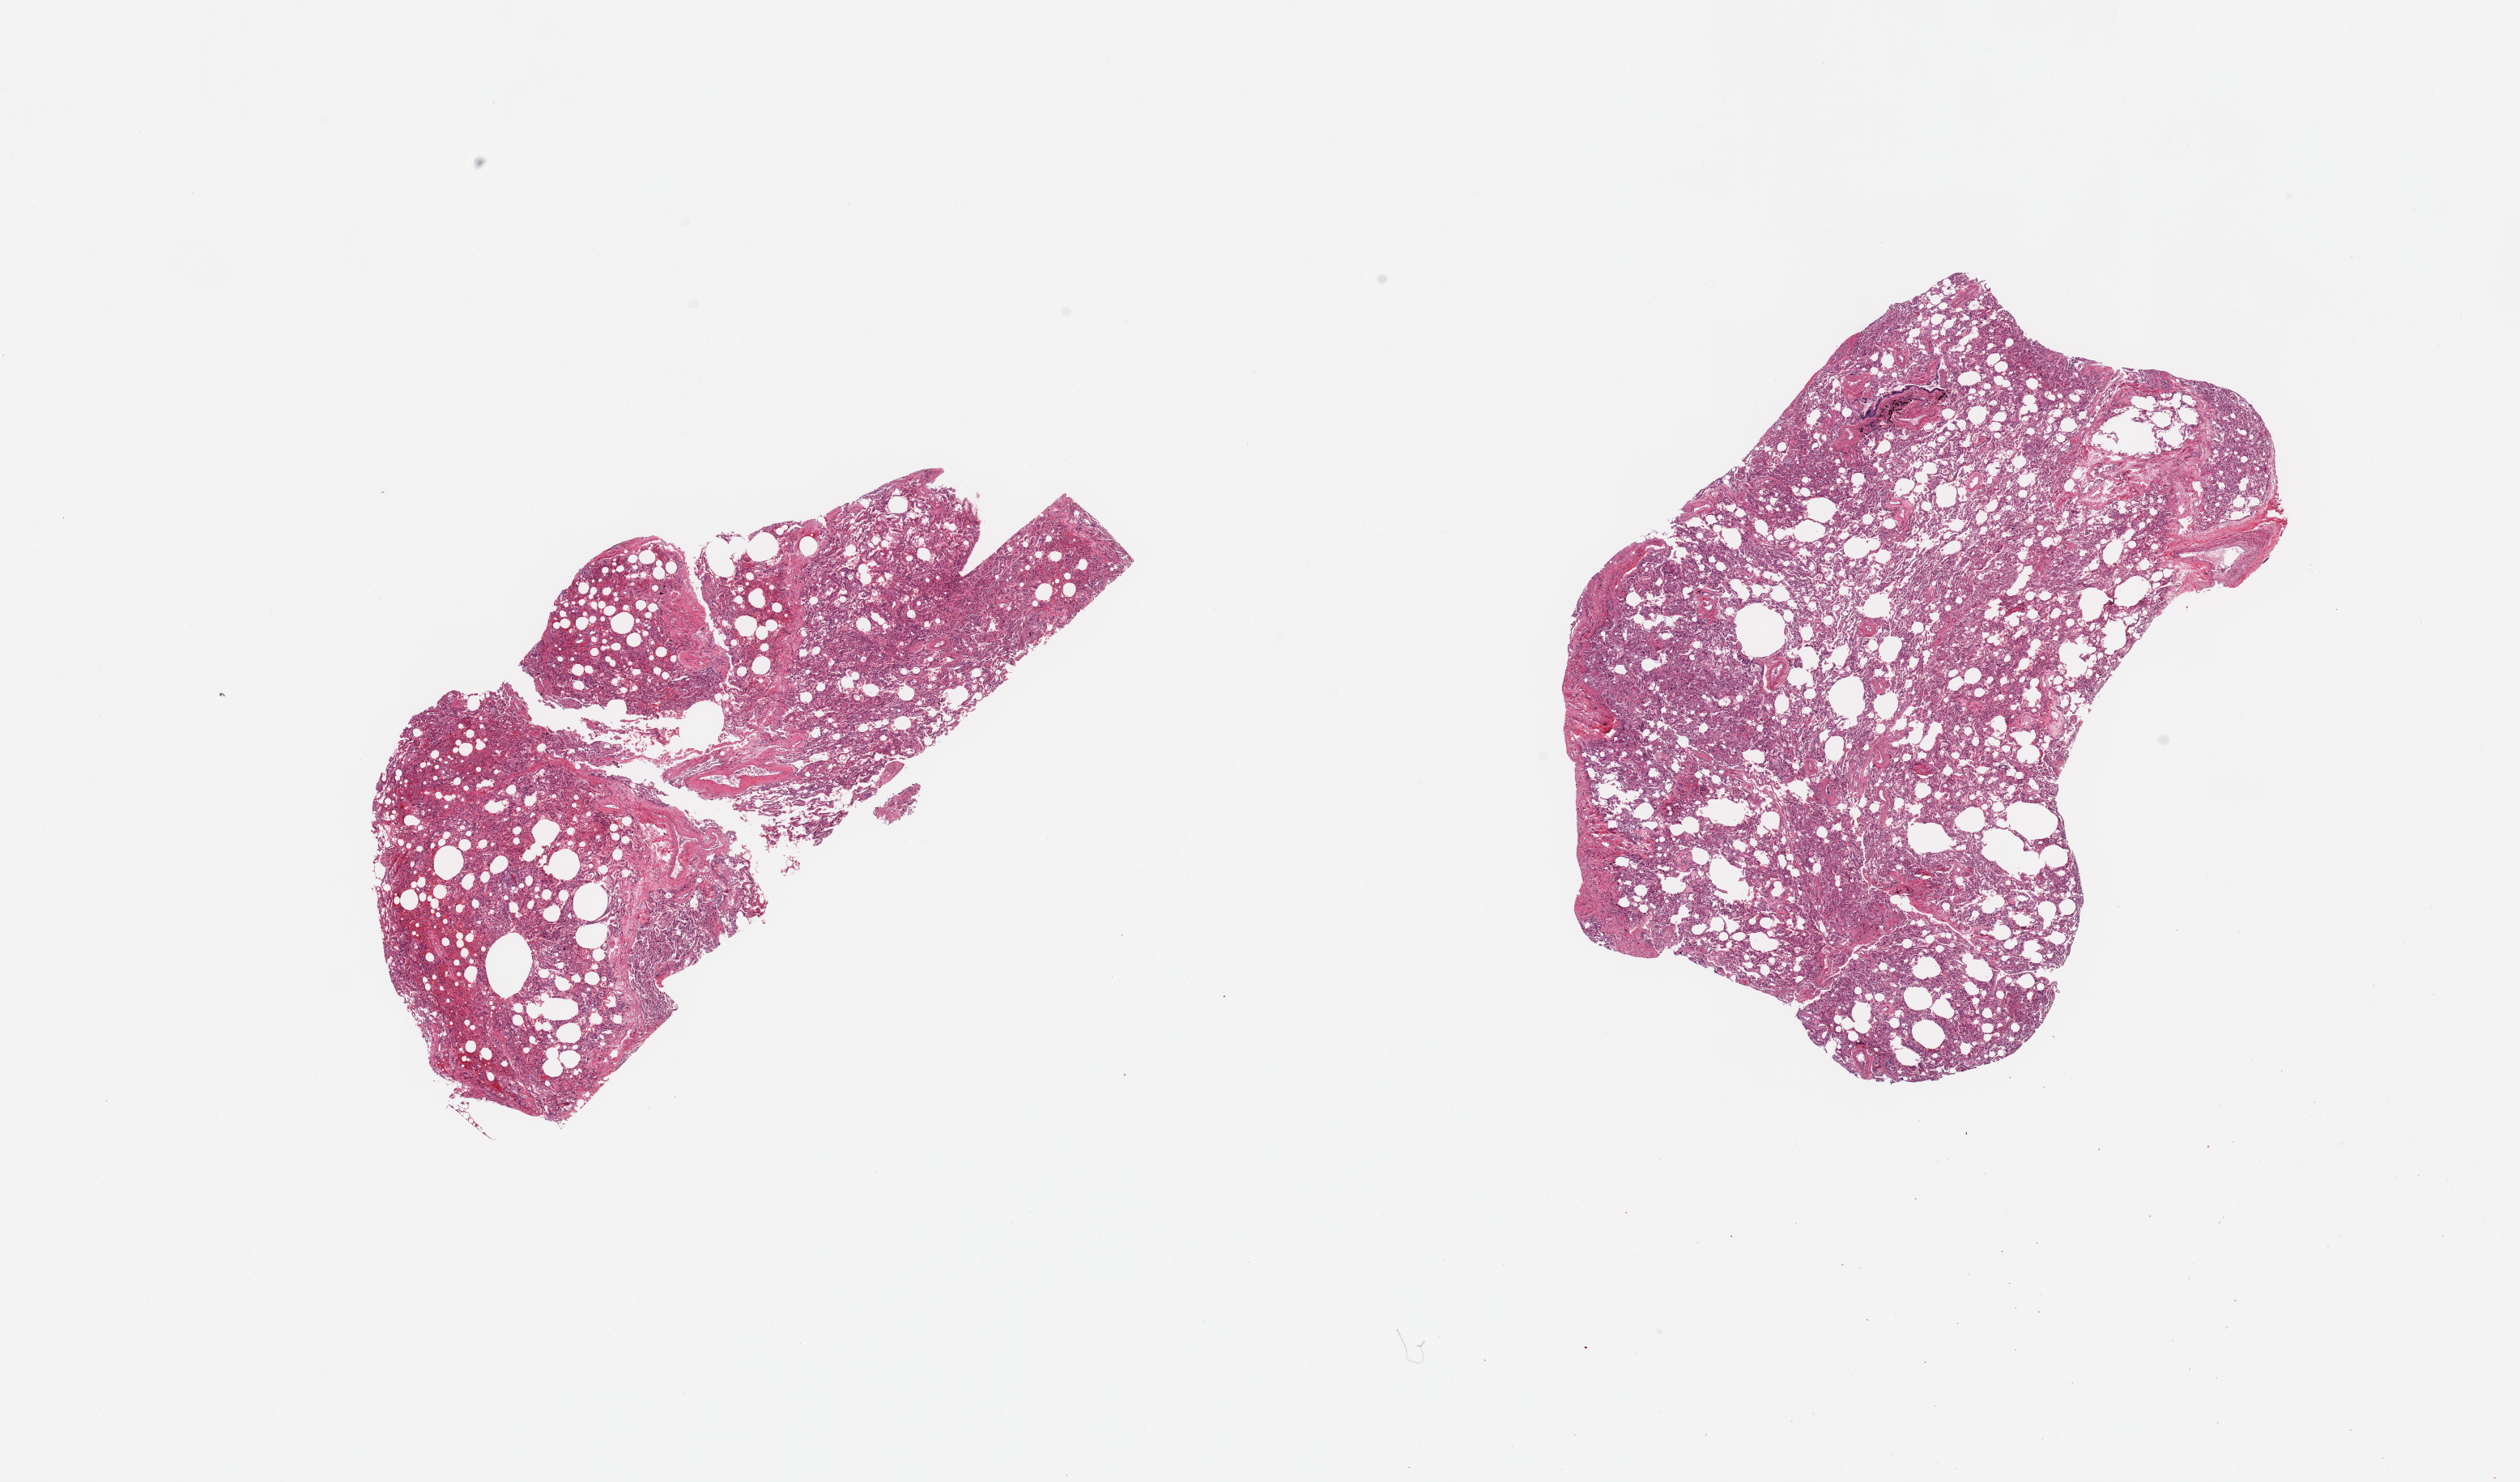
Hematoxylin and eosin (H&E) whole-slide image — a low-resolution overview of the entire scanned area, about 24.6 x 14.5 mm (slide scanned at 20x), PAXgene-fixed, paraffin-embedded tissue, target tissue: lung, donor tissue sample. Male donor.
- review note (as recorded): 2 pieces; focal vascular congestion & hemorrhage